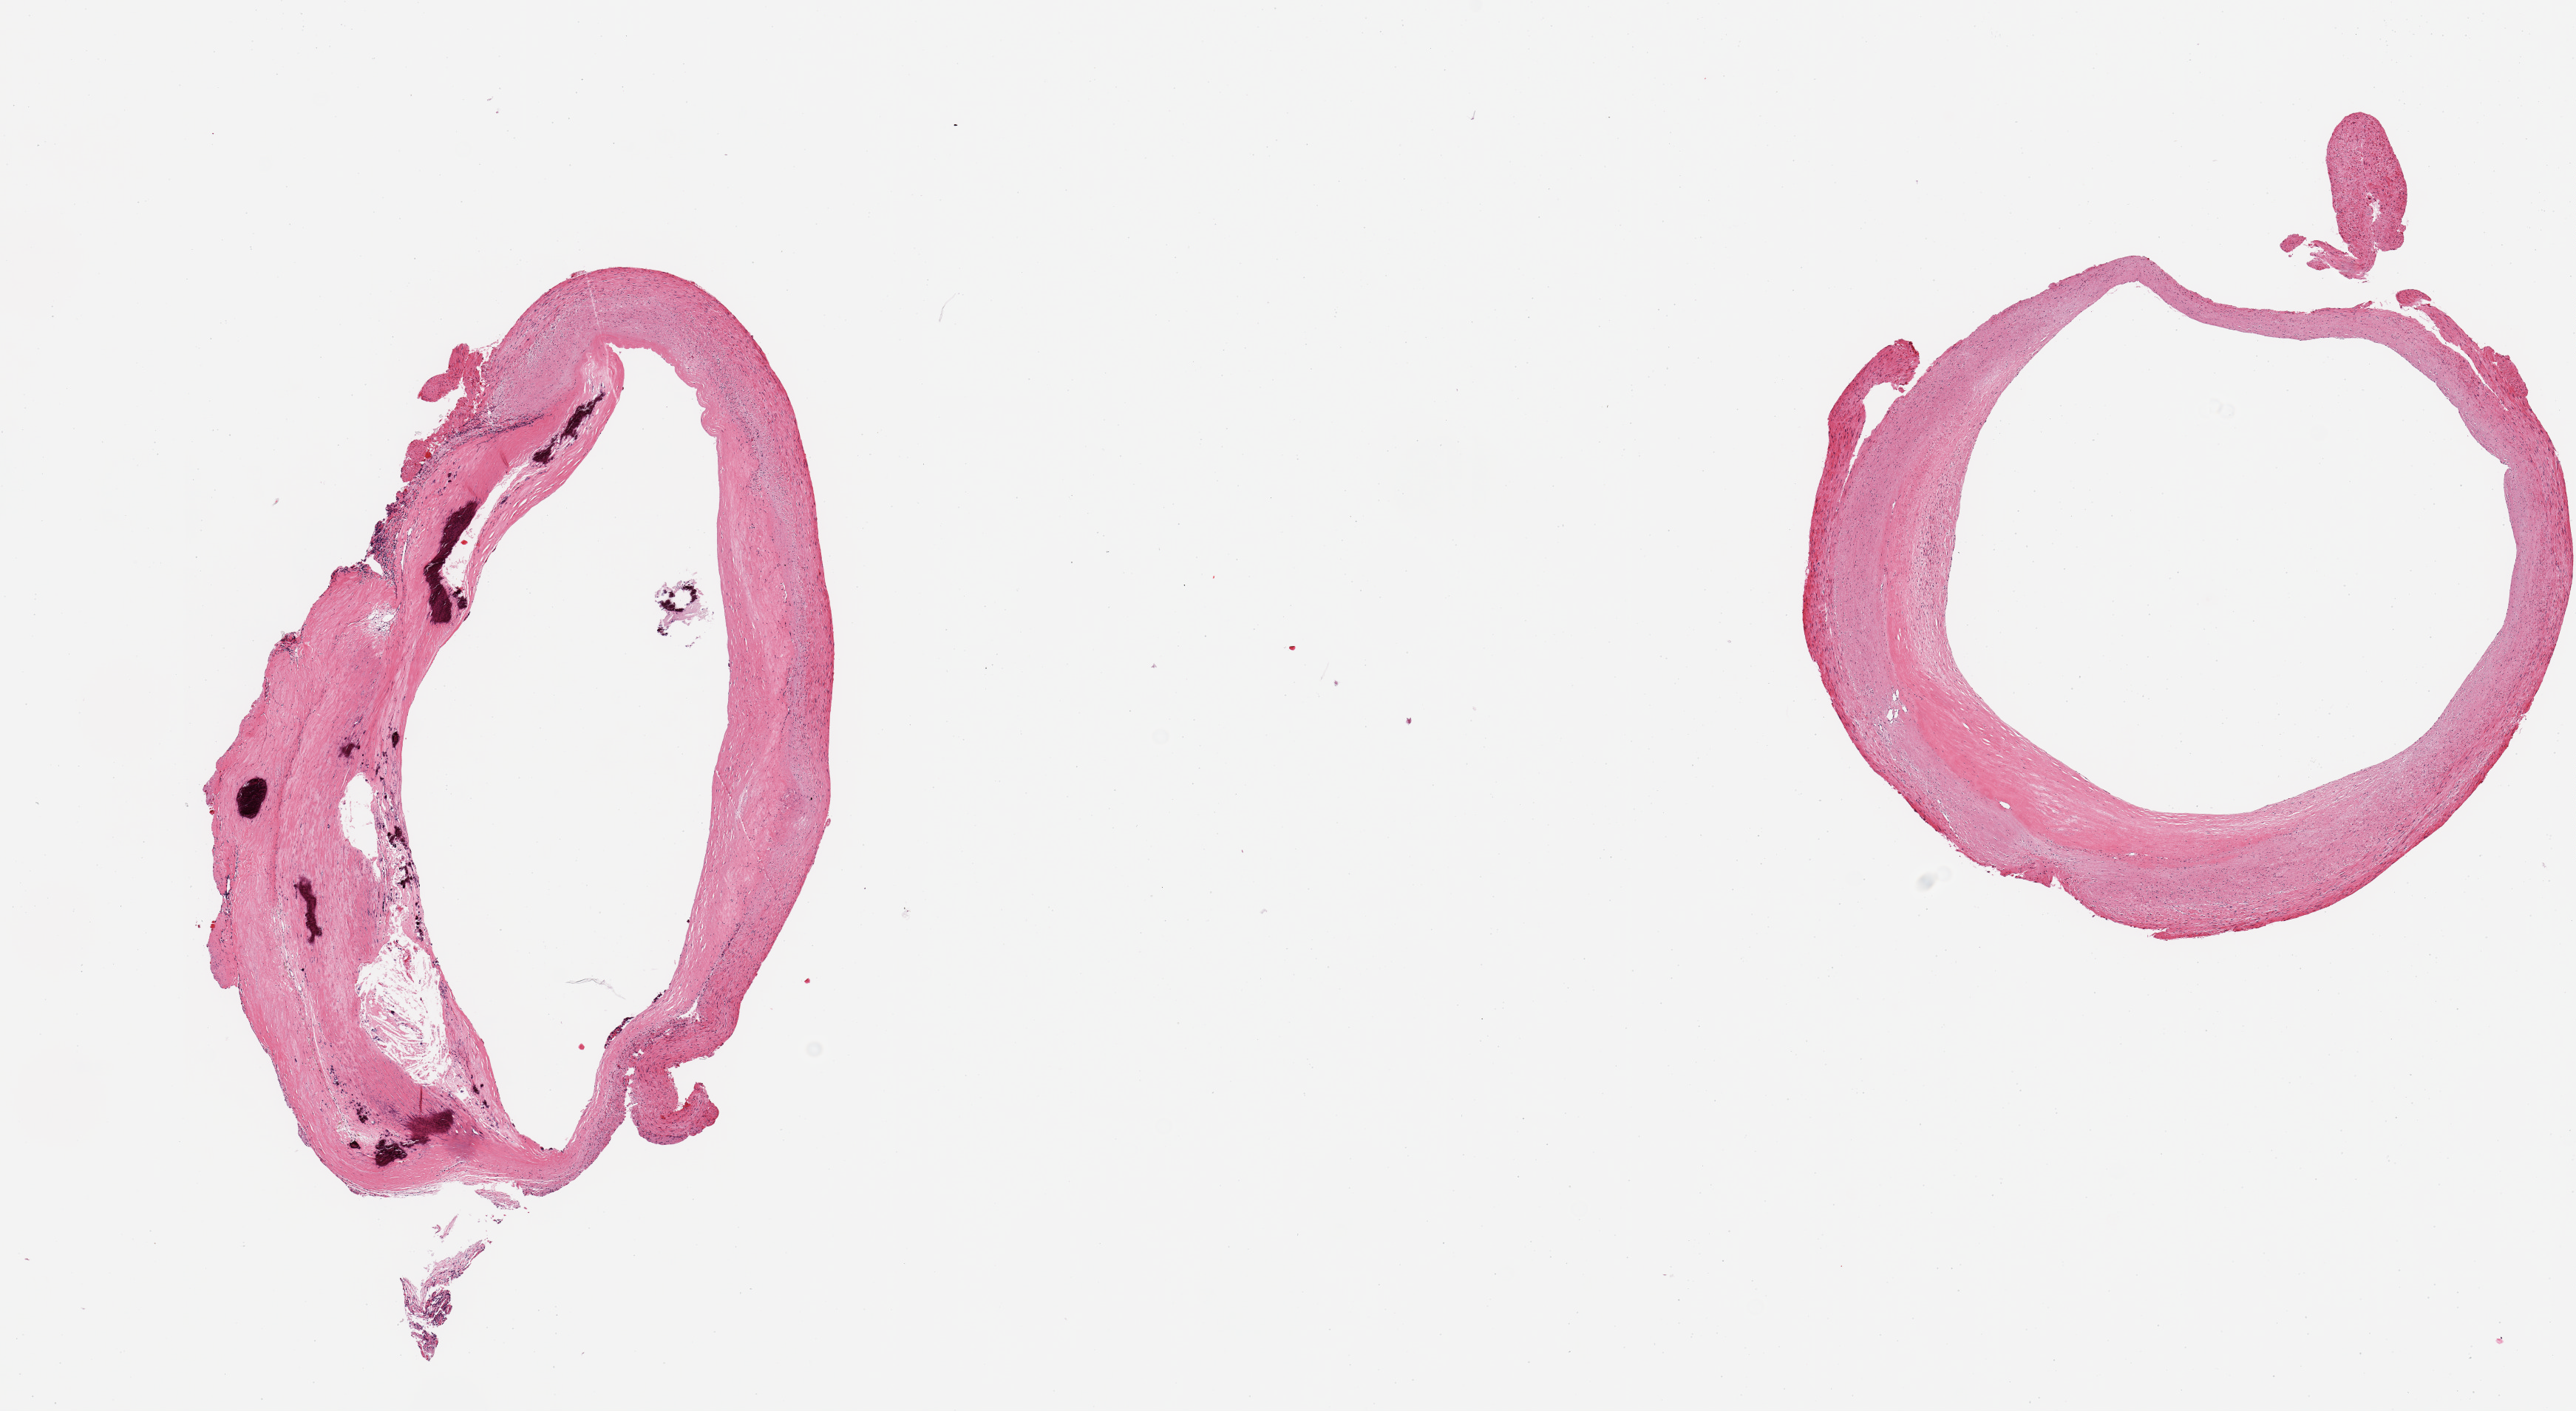
Hematoxylin and eosin (H&E) whole-slide image, brightfield — a low-resolution overview of the entire scanned area, about 13.8 x 7.5 mm. PAXgene-fixed, paraffin-embedded tissue. Section of coronary artery (target tissue). Donor tissue sample.
Review note (as recorded): 2 pieces; moderate intimal fibrous thickening in 1; other has marked atheromatous calcified plaque; well trimmed.